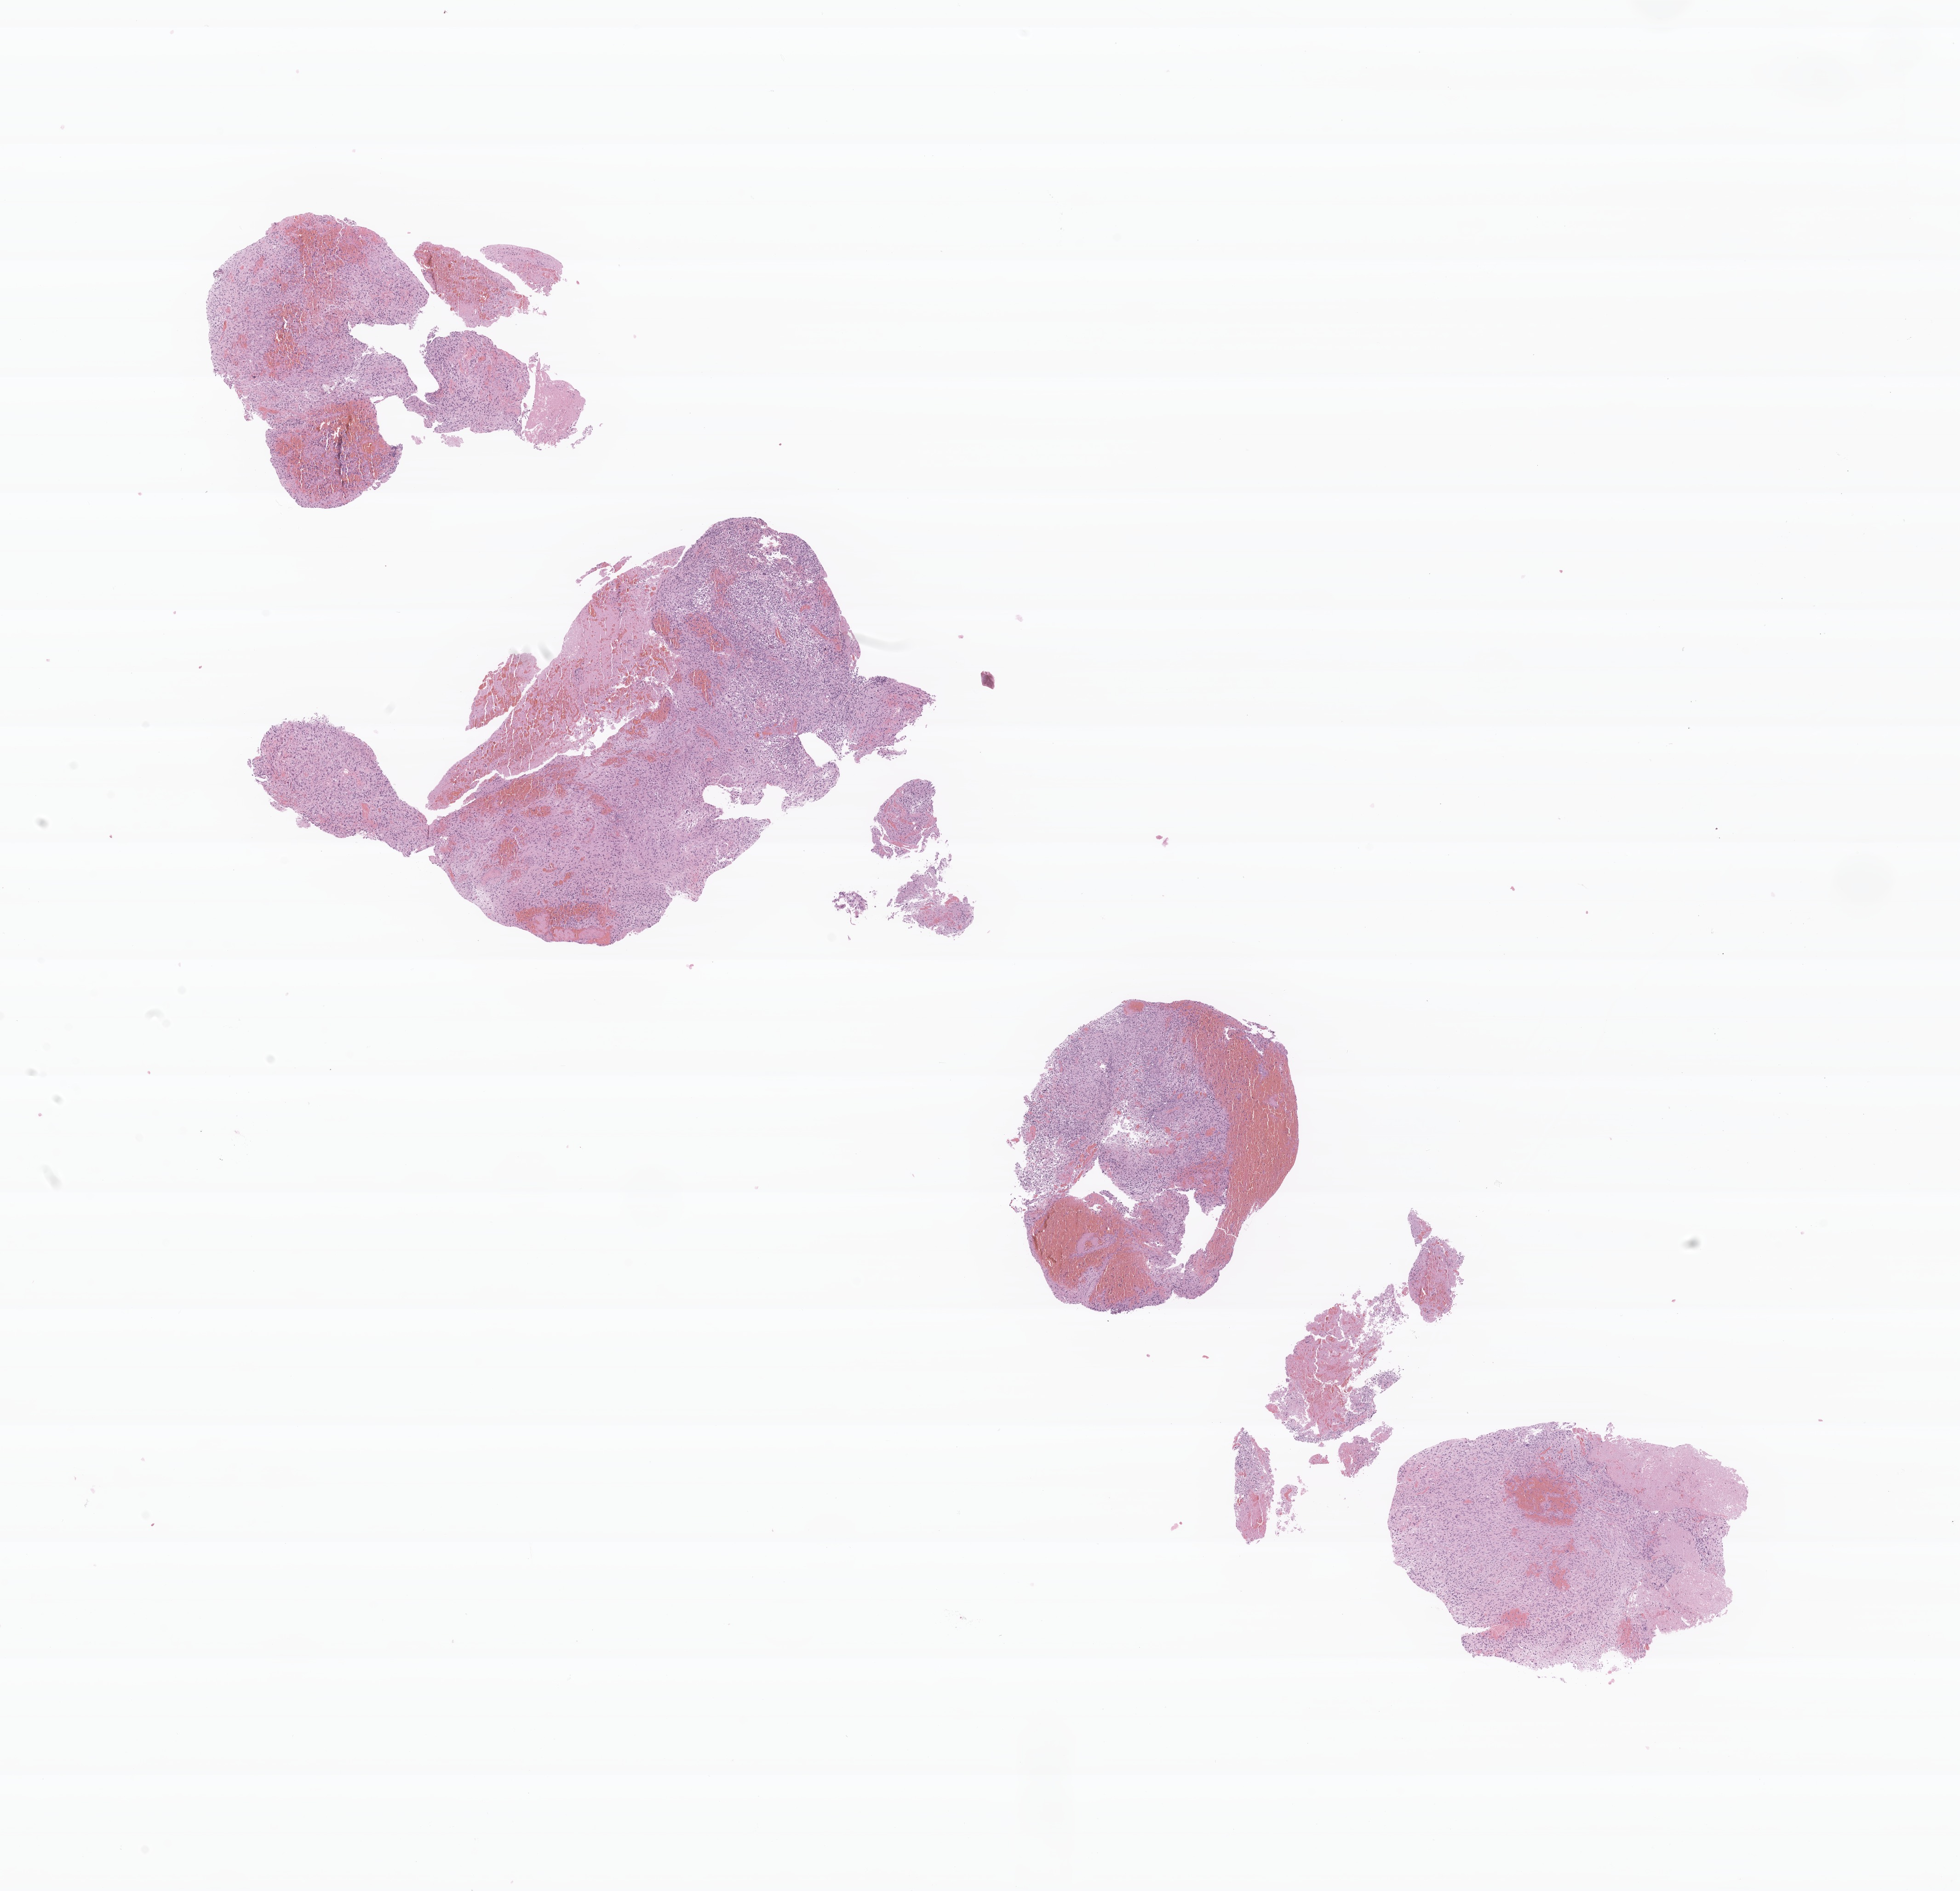
Digitized haematoxylin and eosin-stained section of tumor tissue from the brain, whole scanned area (about 17.9 x 17.3 mm) shown as a low-resolution overview. Formalin-fixed, paraffin-embedded (FFPE) tissue. Male patient, age 60 months (5 years).
Diagnosis (ICD-O-3 morphology term): Neoplasm, malignant.